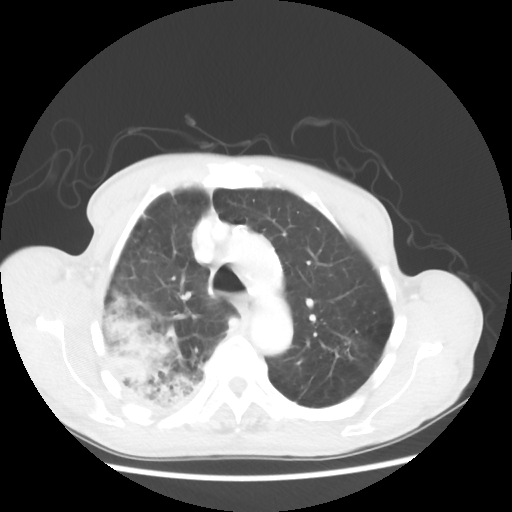
Chest CT, one axial slice; slice 41 of 58 in the series (ordered by position); reconstruction kernel STANDARD; 100 kVp; lung window (W 1500 / L -600 HU); 5 mm slice thickness; 512 × 512 image matrix, field of view 351 × 351 mm. Patient: male, 75 years. From the clinical record (not read from this slice): clinical TNM (as recorded): T4 N1 M1.
Annotated regions visible in this slice (bounding box drawn by a radiologist):
- lung tumour (recorded histology: adenocarcinoma): box from (x=87, y=289) to (x=208, y=406) px